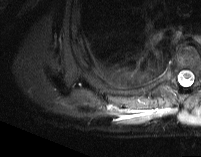
MRI of an extremity soft-tissue mass, one axial slice. Slice 12 of 74 in the series (ordered by position). STIR. MR volume resampled by the dataset authors to the PET/CT grid (not the native acquisition matrix). 3.27 mm slice thickness. 201 × 157 image matrix, field of view 196 × 153 mm. Male patient. Case-level facts recorded for this patient, not image findings: histological type: pleiomorphic spindle cell undifferentiated; grade: high; site of the primary tumour: right parascapusular.
Structures marked on this image (expert contour drawn on MRI and transferred to this co-registered scan by the dataset authors):
- gross tumour volume including surrounding oedema: bounding box <110,107,150,120> (left, top, right, bottom; pixels)